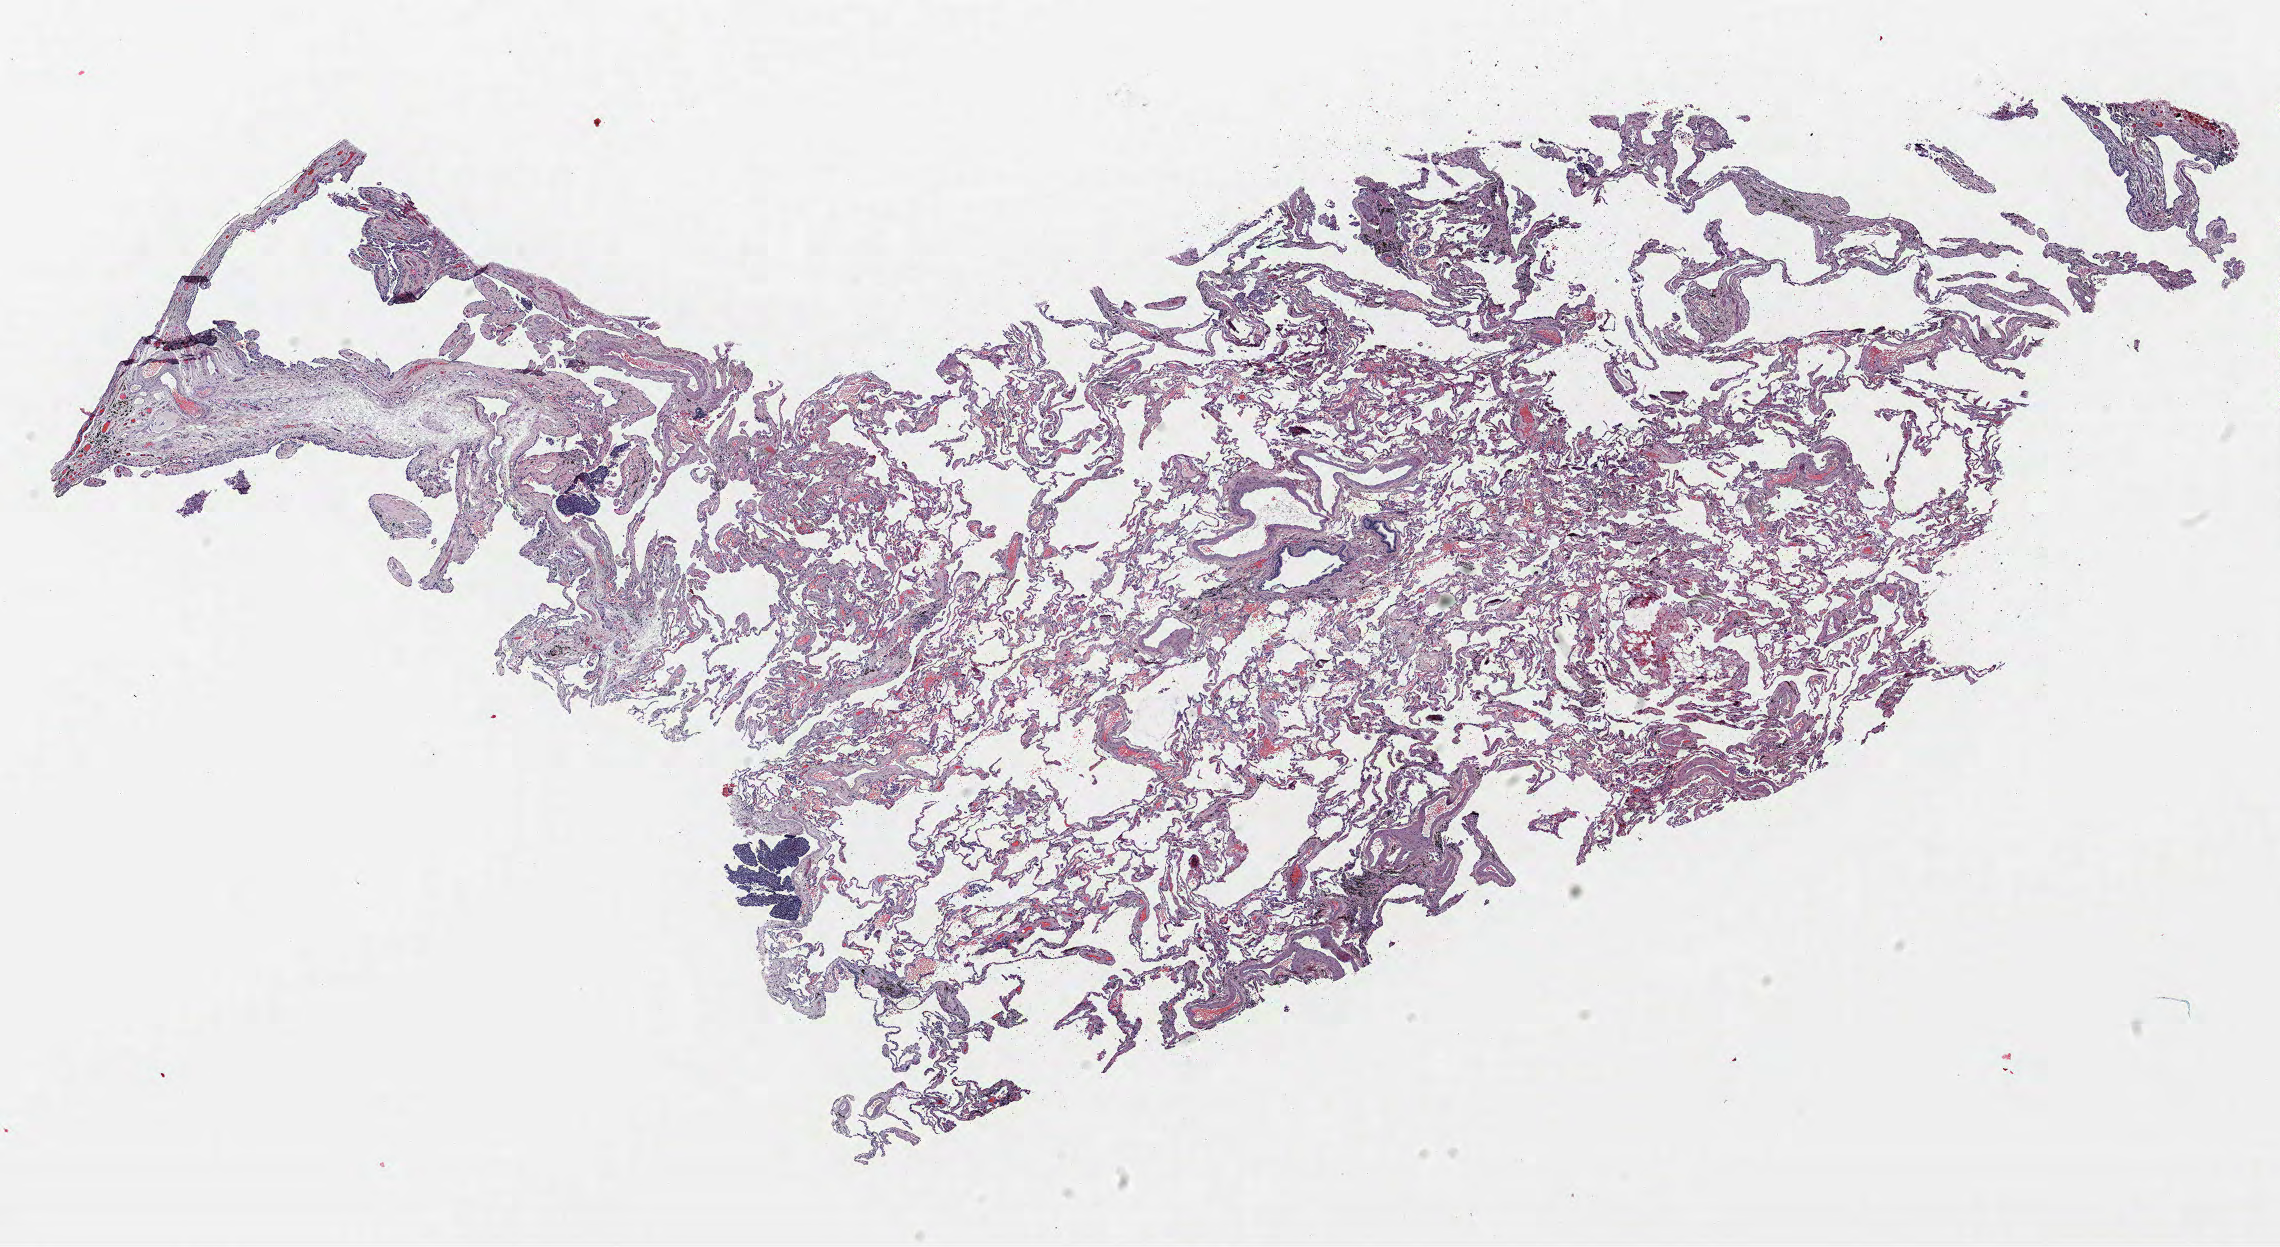
Whole-slide histology image, Hematoxylin and eosin (H&E) stained, shown as a low-resolution overview of the whole scanned area (about 18.2 x 10.0 mm, acquisition: 40x scan). FFPE section. Lung tissue. Male, age 65 at enrolment. Former smoker at enrolment. Grade: moderately differentiated (G2).
- primary tumour location (clinical record): right upper lobe
- tumour size (pathology): 16 mm
- participant's lung-cancer diagnosis: Squamous cell carcinoma, NOS
- stage (AJCC 6th edition): IA